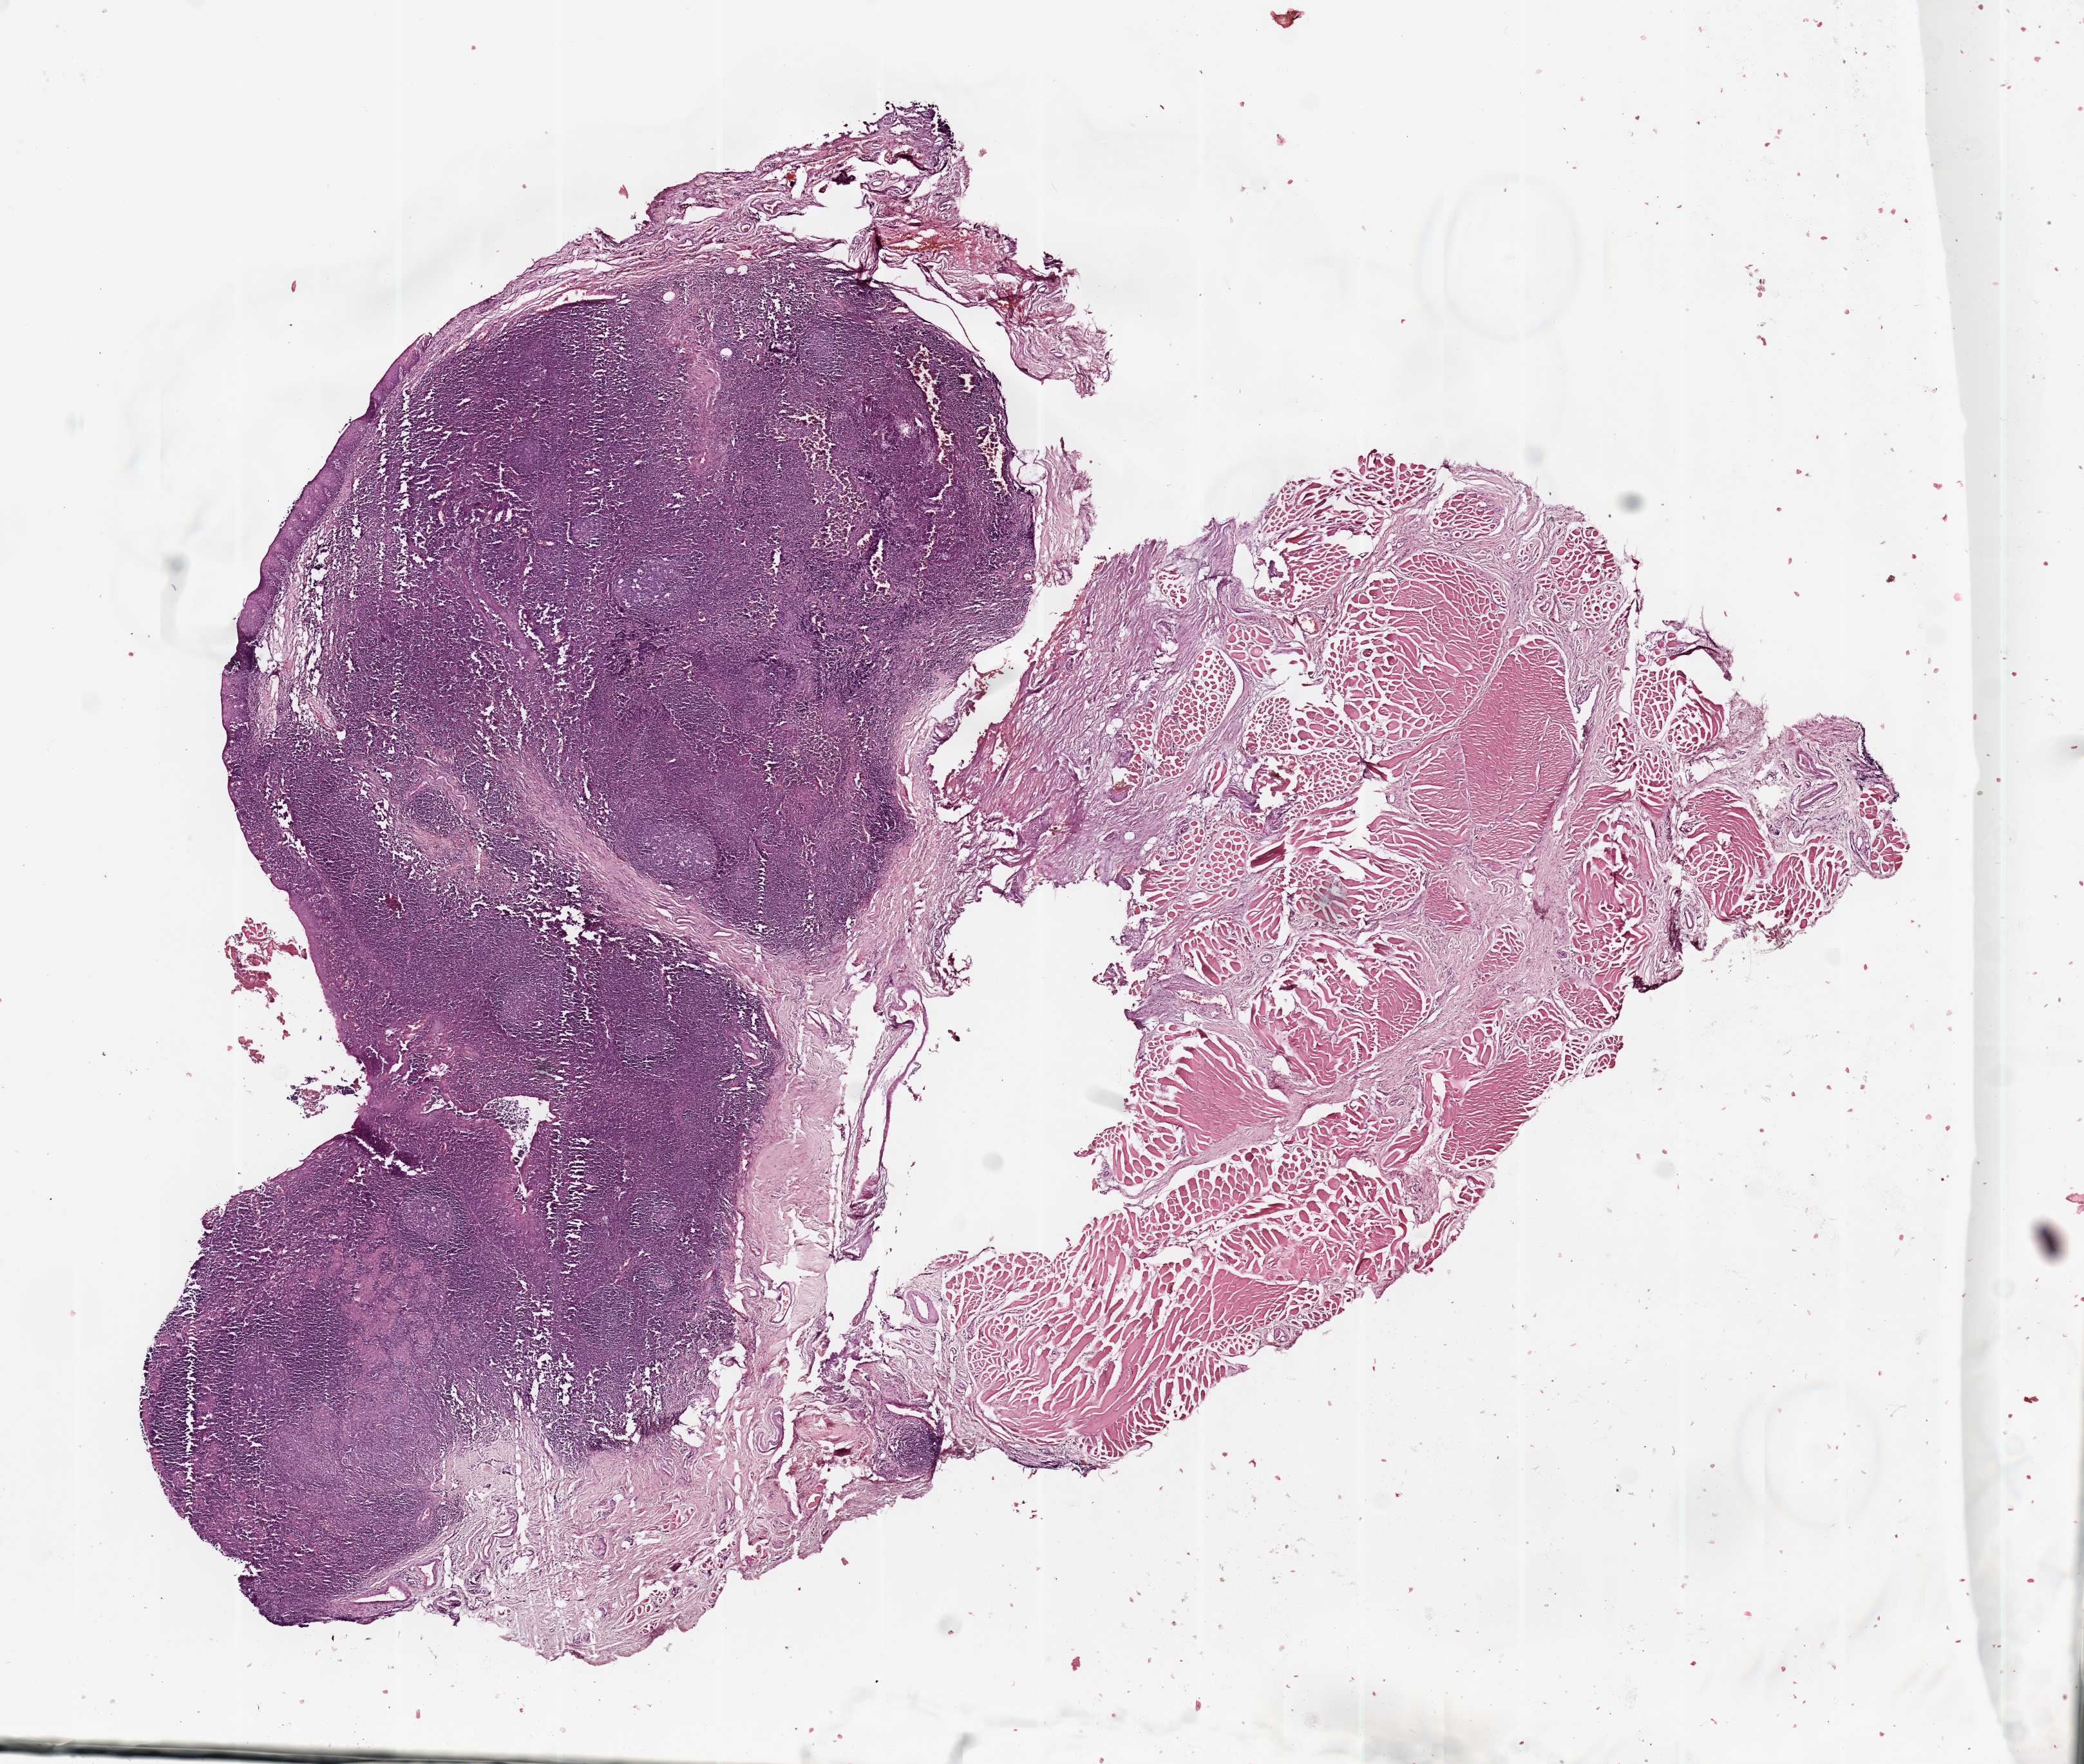
Whole-slide histology image, Hematoxylin and eosin (H&E) stained, low-resolution overview of the scanned area, about 12.8 x 10.8 mm; head and neck, tissue type not recorded. 51-year-old male patient.
- patient diagnosis: Squamous cell carcinoma, NOS (oropharynx, NOS)